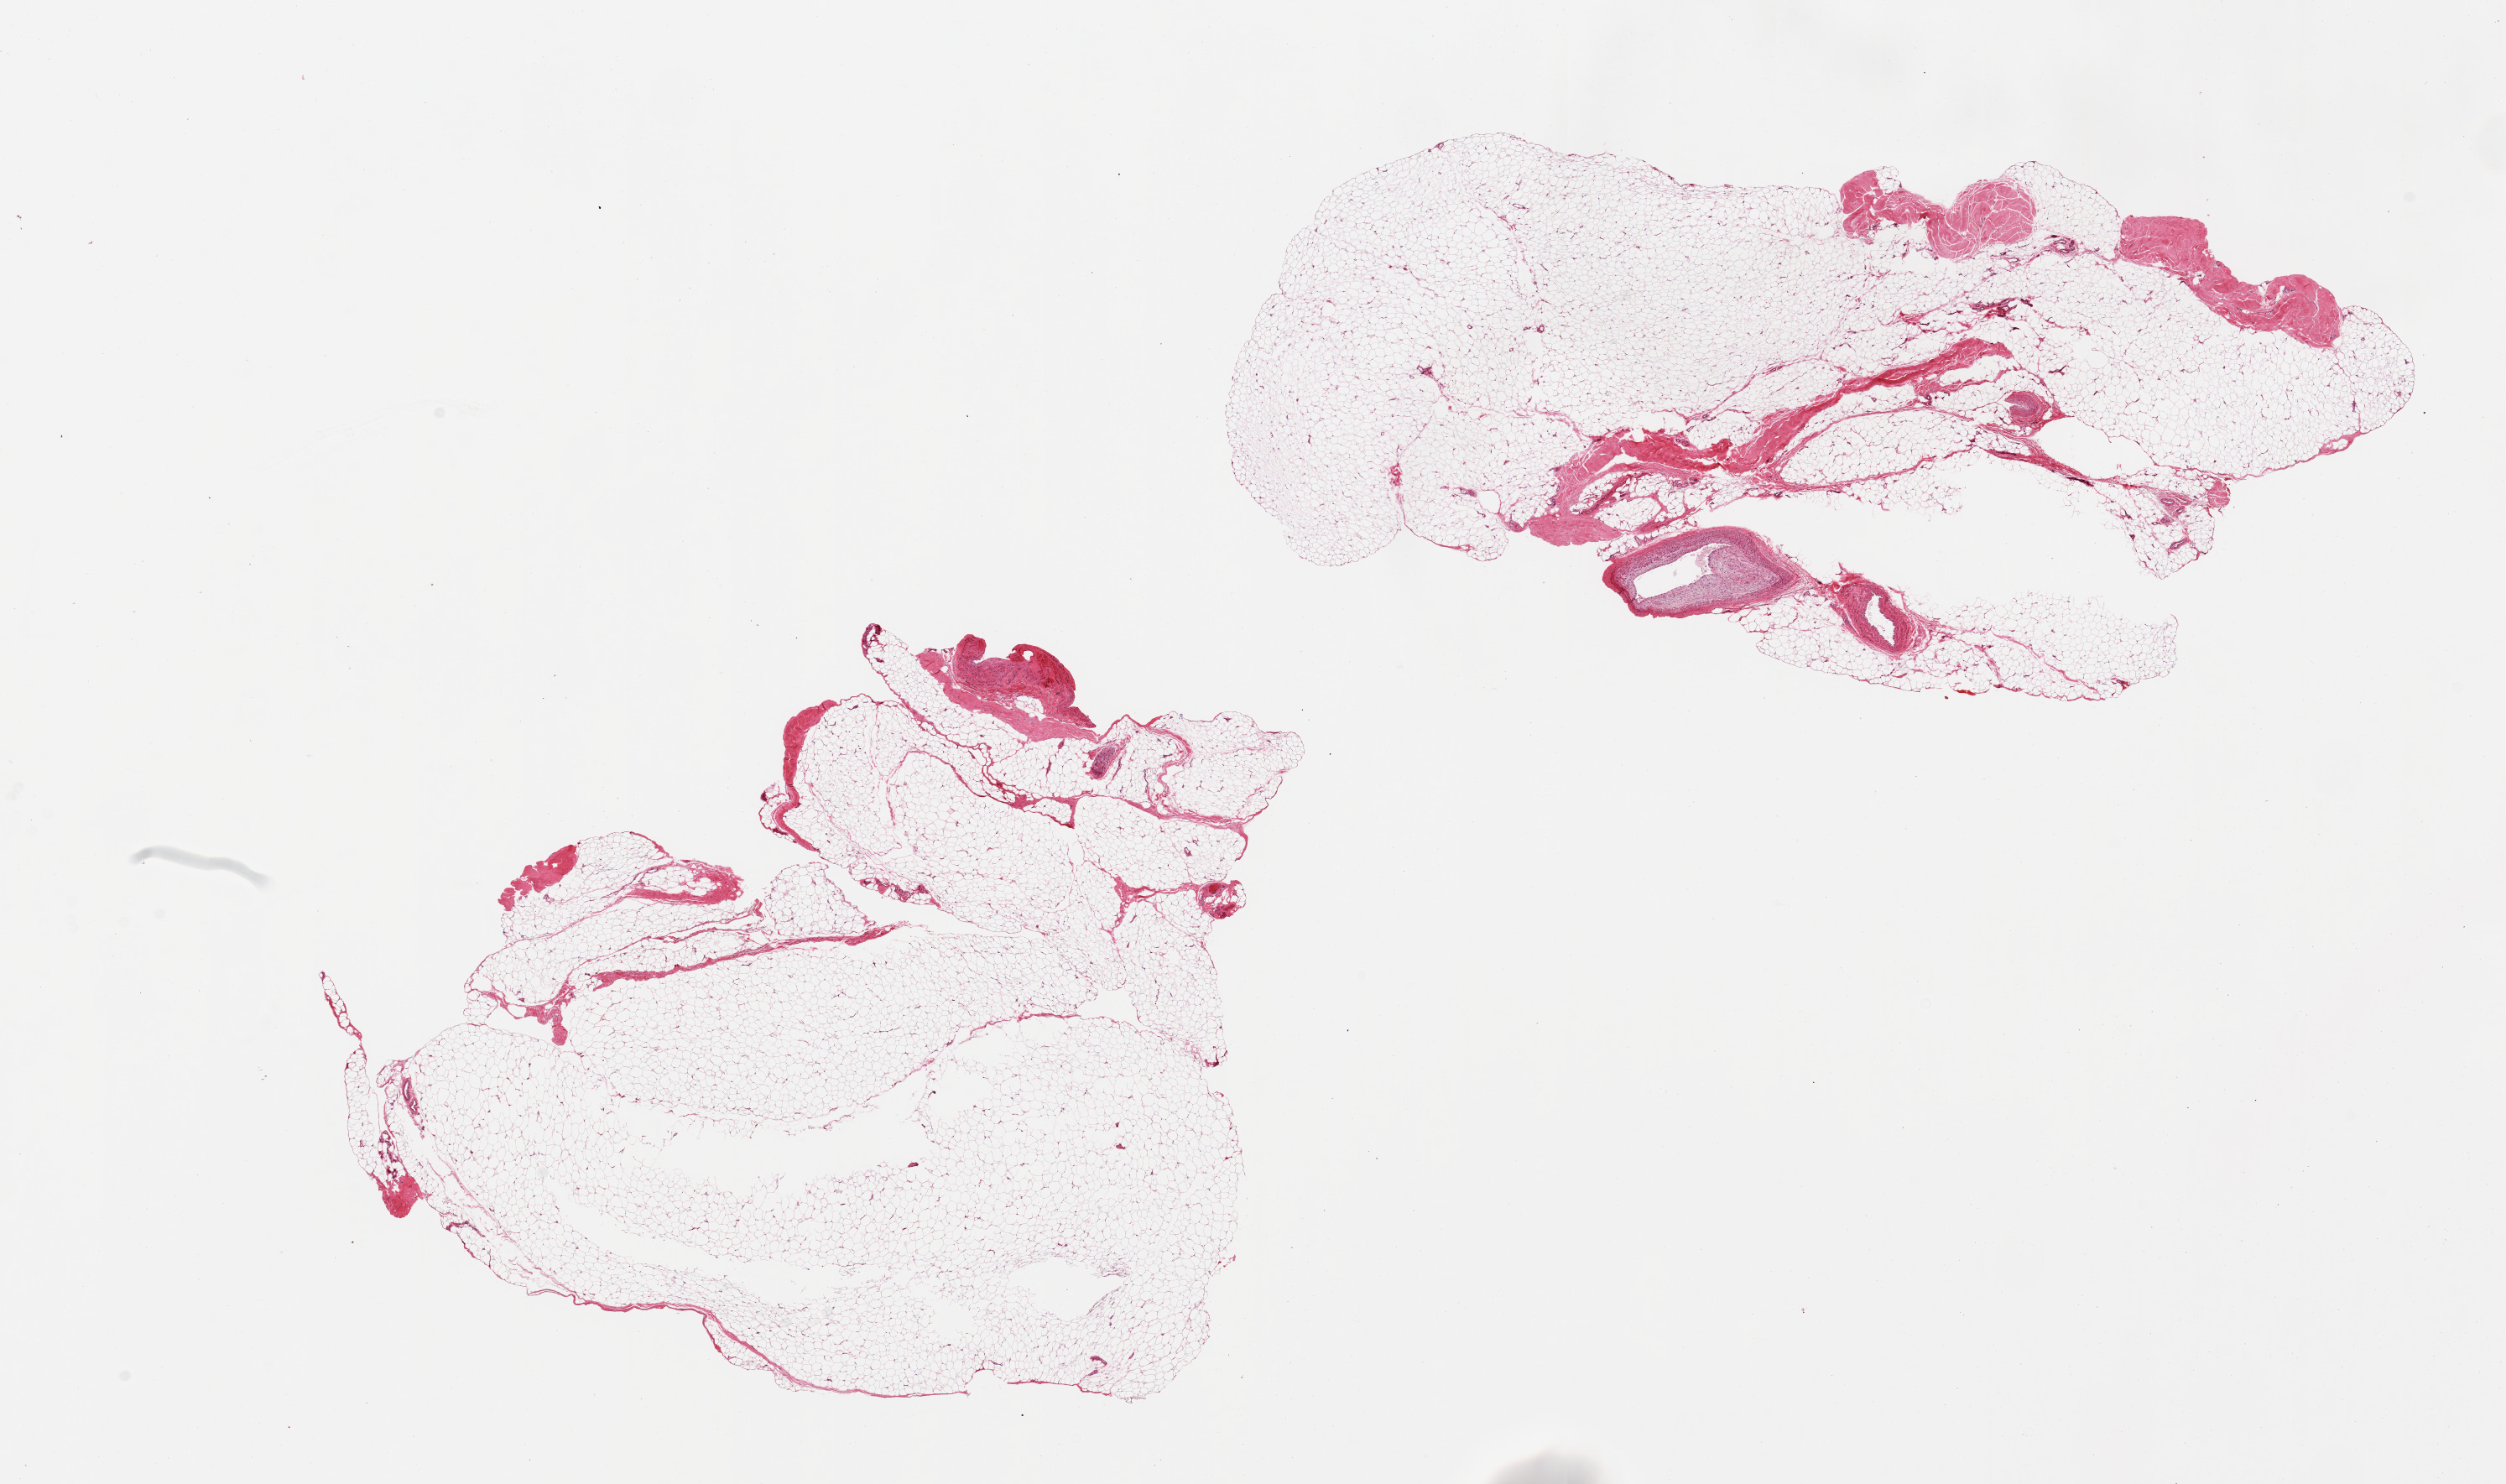
Haematoxylin and eosin whole-slide image — low-resolution overview of the scanned area, about 23.6 x 14.0 mm; PAXgene-fixed paraffin-embedded (PFPE) section; target tissue: adipose tissue; tissue donor sample. Male donor.
Pathologist's review note for this sample: 2 pieces, ~5-10% fascia/vascular elements.